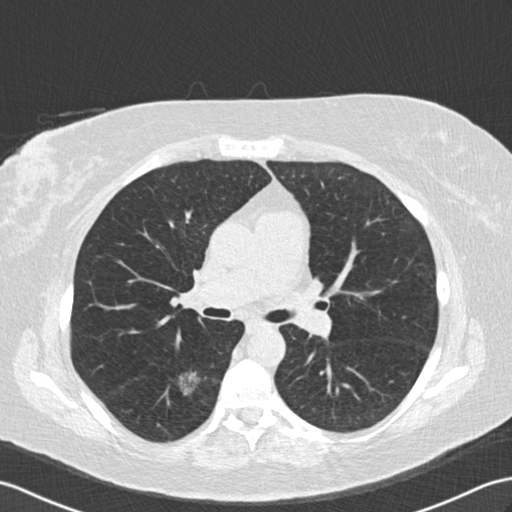
Chest CT (low-dose screening protocol), one axial image, second annual screen, lung window (W 1500 / L -600 HU), 2 mm slice thickness. Female participant, aged 65 years at enrolment. Former smoker at enrolment.
• Expert reader's lesion annotation, box from (x=157, y=355) to (x=213, y=411) px.
• Reader record for this screening exam (exam-level; its link to the box is not recorded): non-calcified nodule or mass ≥4 mm, right lower lobe, 18 × 16 mm, spiculated (stellate) margins, soft tissue attenuation, pre-existing on the prior screen: yes; interval growth: yes.
• Participant outcome: lung cancer diagnosed 239 days after this screen — adenocarcinoma, NOS, right lower lobe, moderately differentiated (G2), stage IA (AJCC 6th edition), 25 mm at pathology.